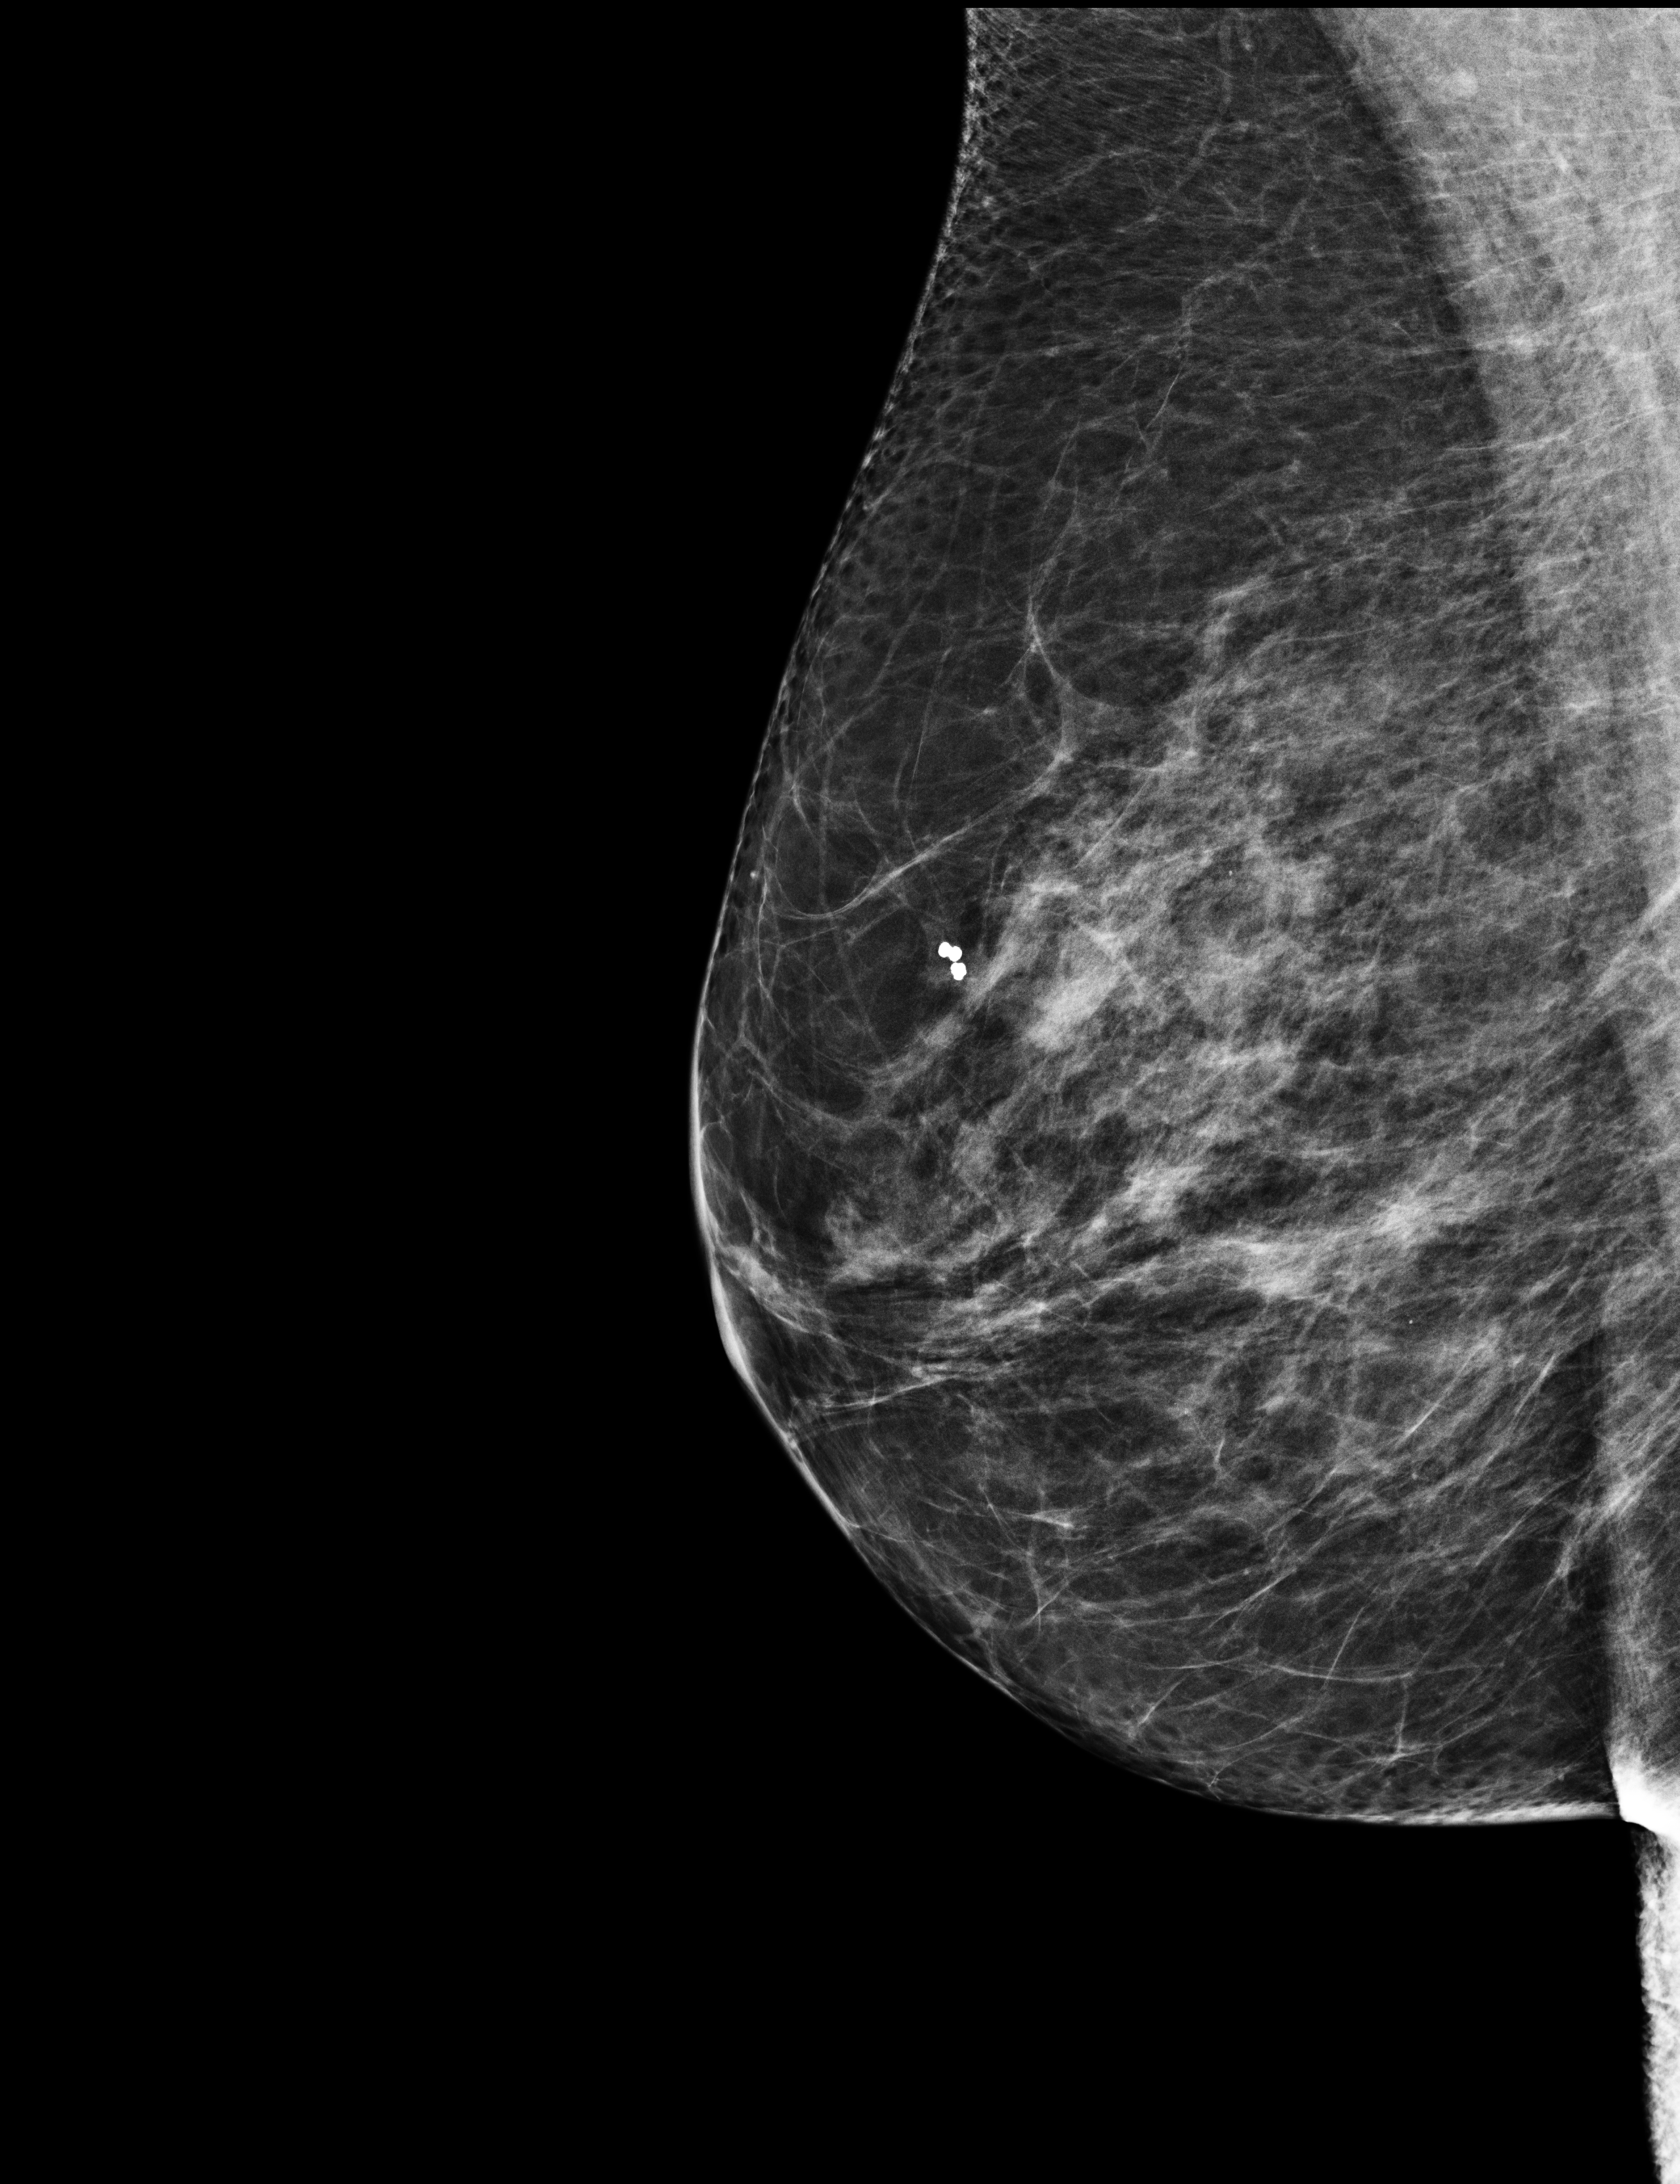
Digital mammogram (FFDM); right breast; mediolateral oblique (MLO) view; screening examination; compressed breast thickness 58 mm. Patient: female, 67 years.
BI-RADS breast density category at the screening exam (both breasts, scale 1–4): 3. Final BI-RADS category for the screening round (tomosynthesis exam, both breasts): category 2. Recall: no recall after this screen.